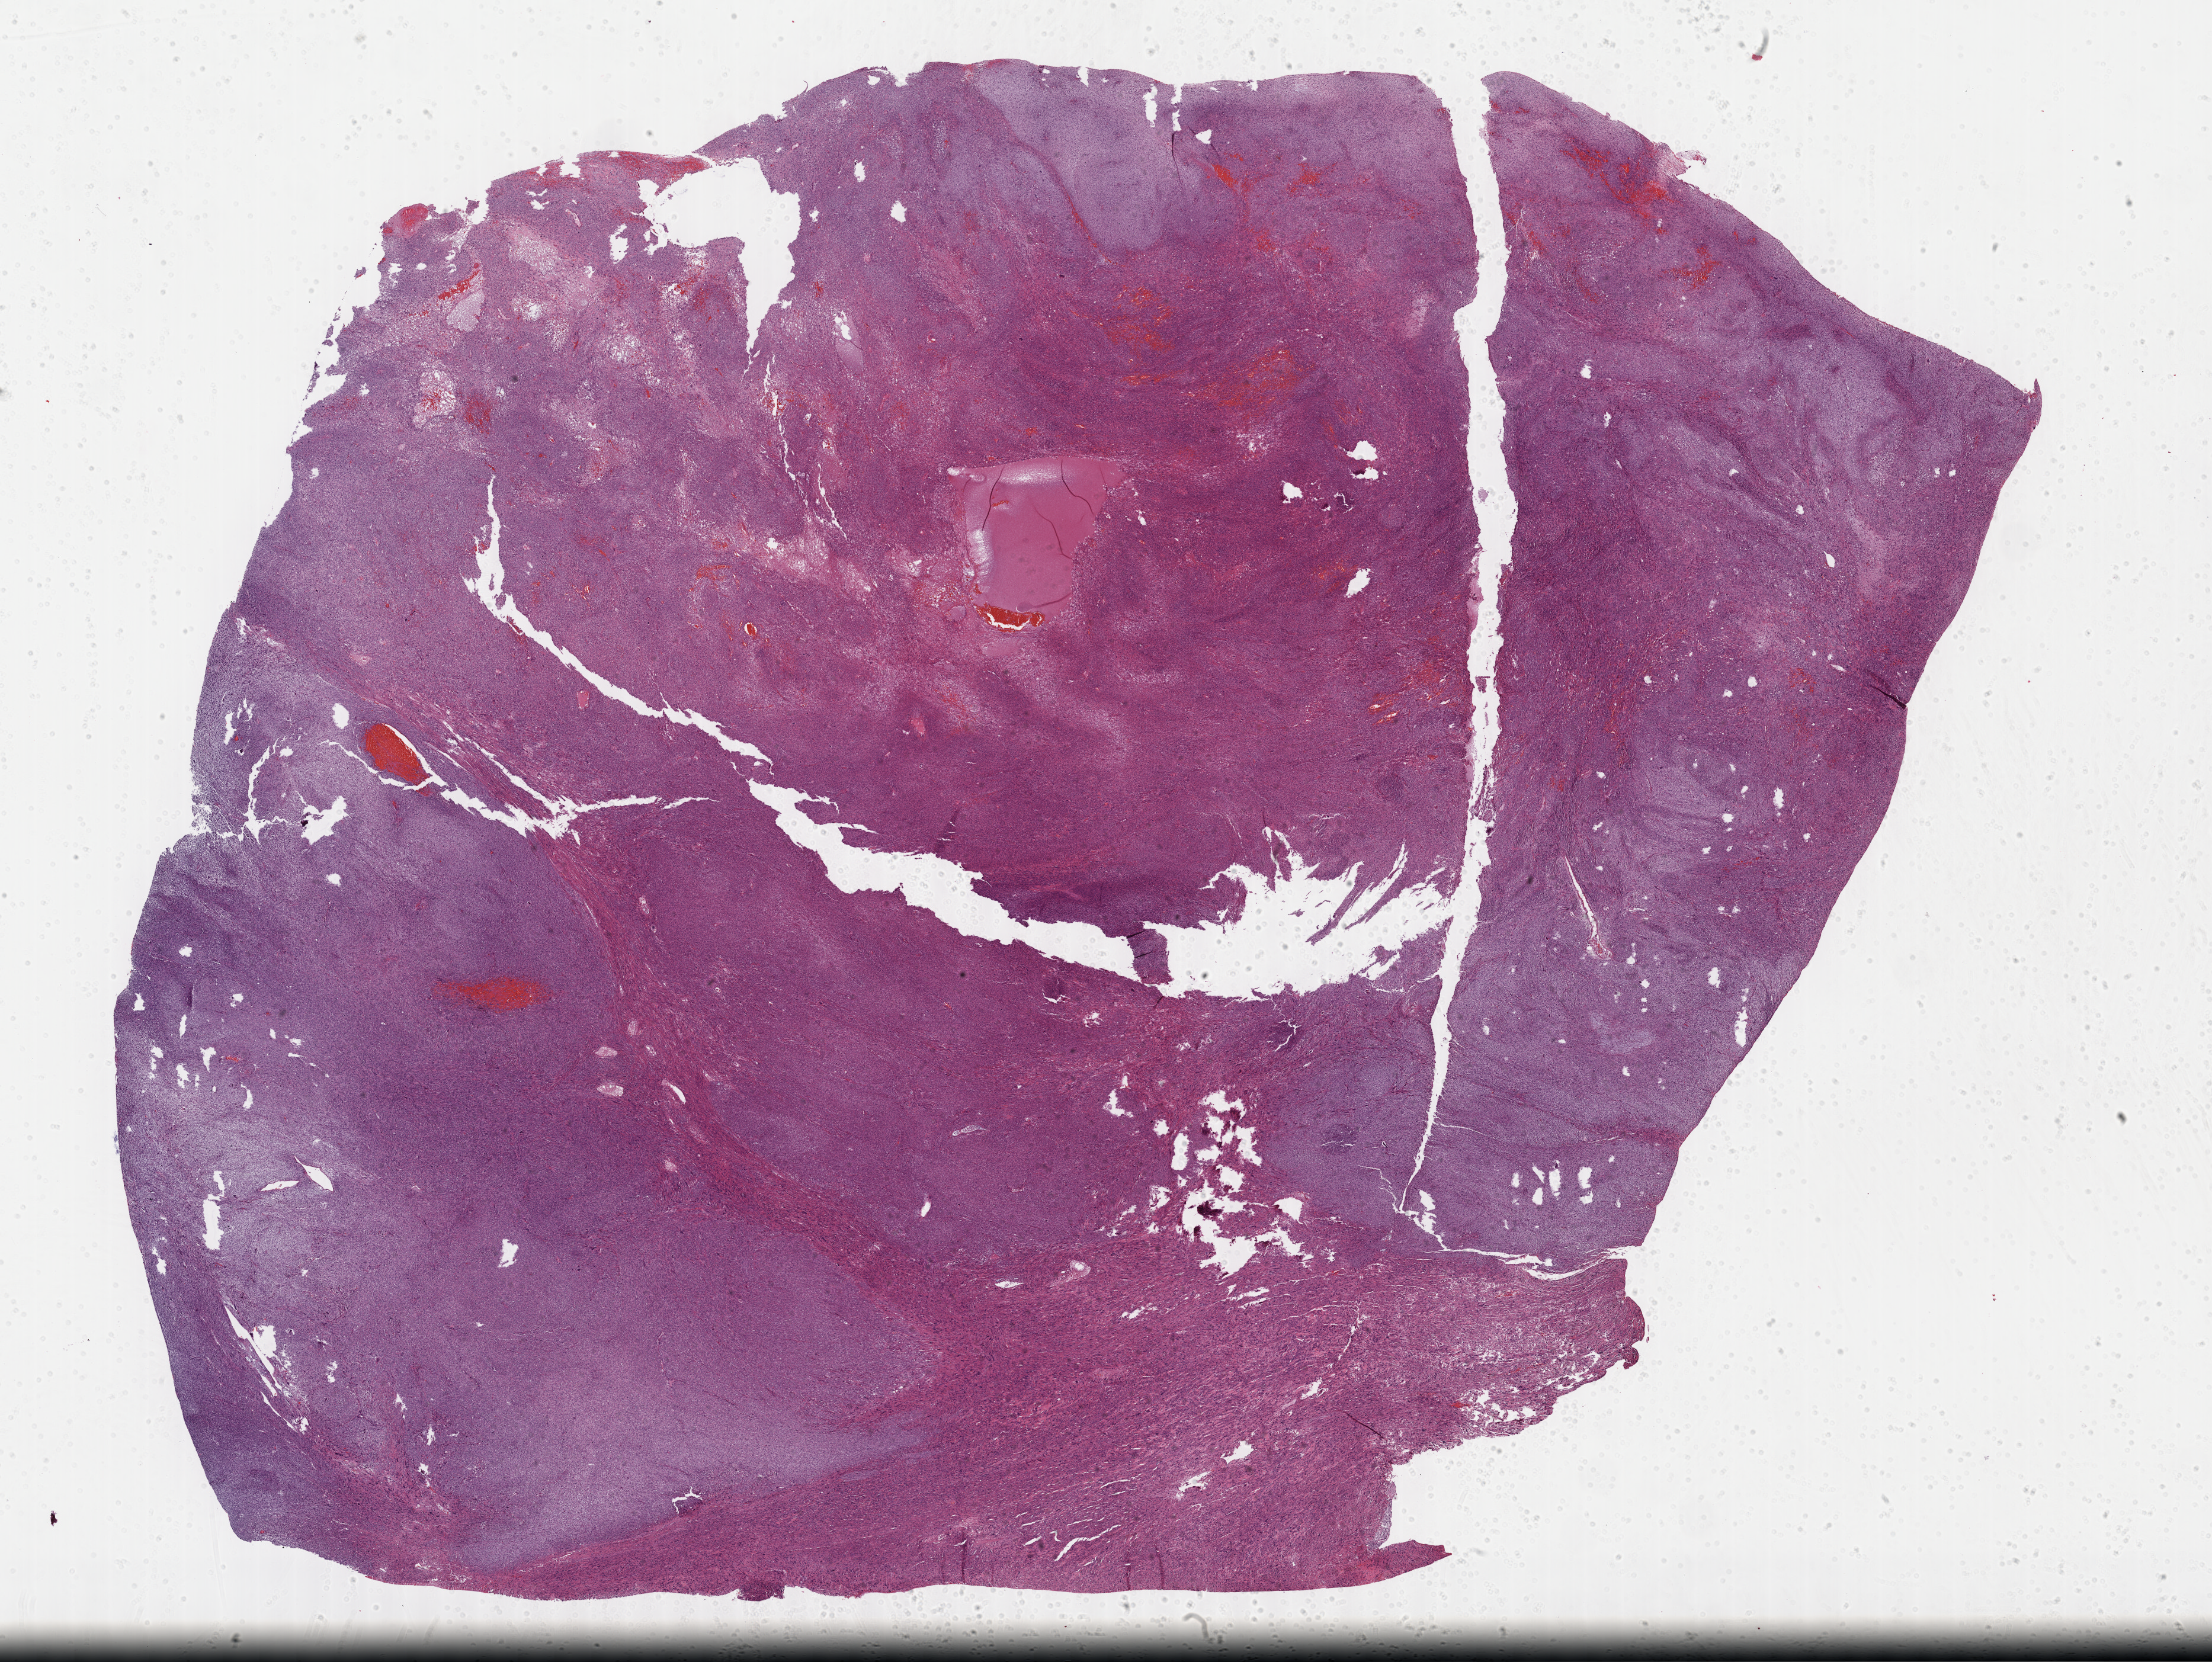
Whole-slide histology image, Hematoxylin and eosin (H&E) stained, low-resolution overview of the scanned area, about 30.2 x 22.7 mm (from a 40x scan); formalin-fixed paraffin-embedded (FFPE) diagnostic section; uterus, primary tumour sample. Patient: female, age at initial diagnosis 43 years.
Diagnosis: Leiomyosarcoma, NOS.